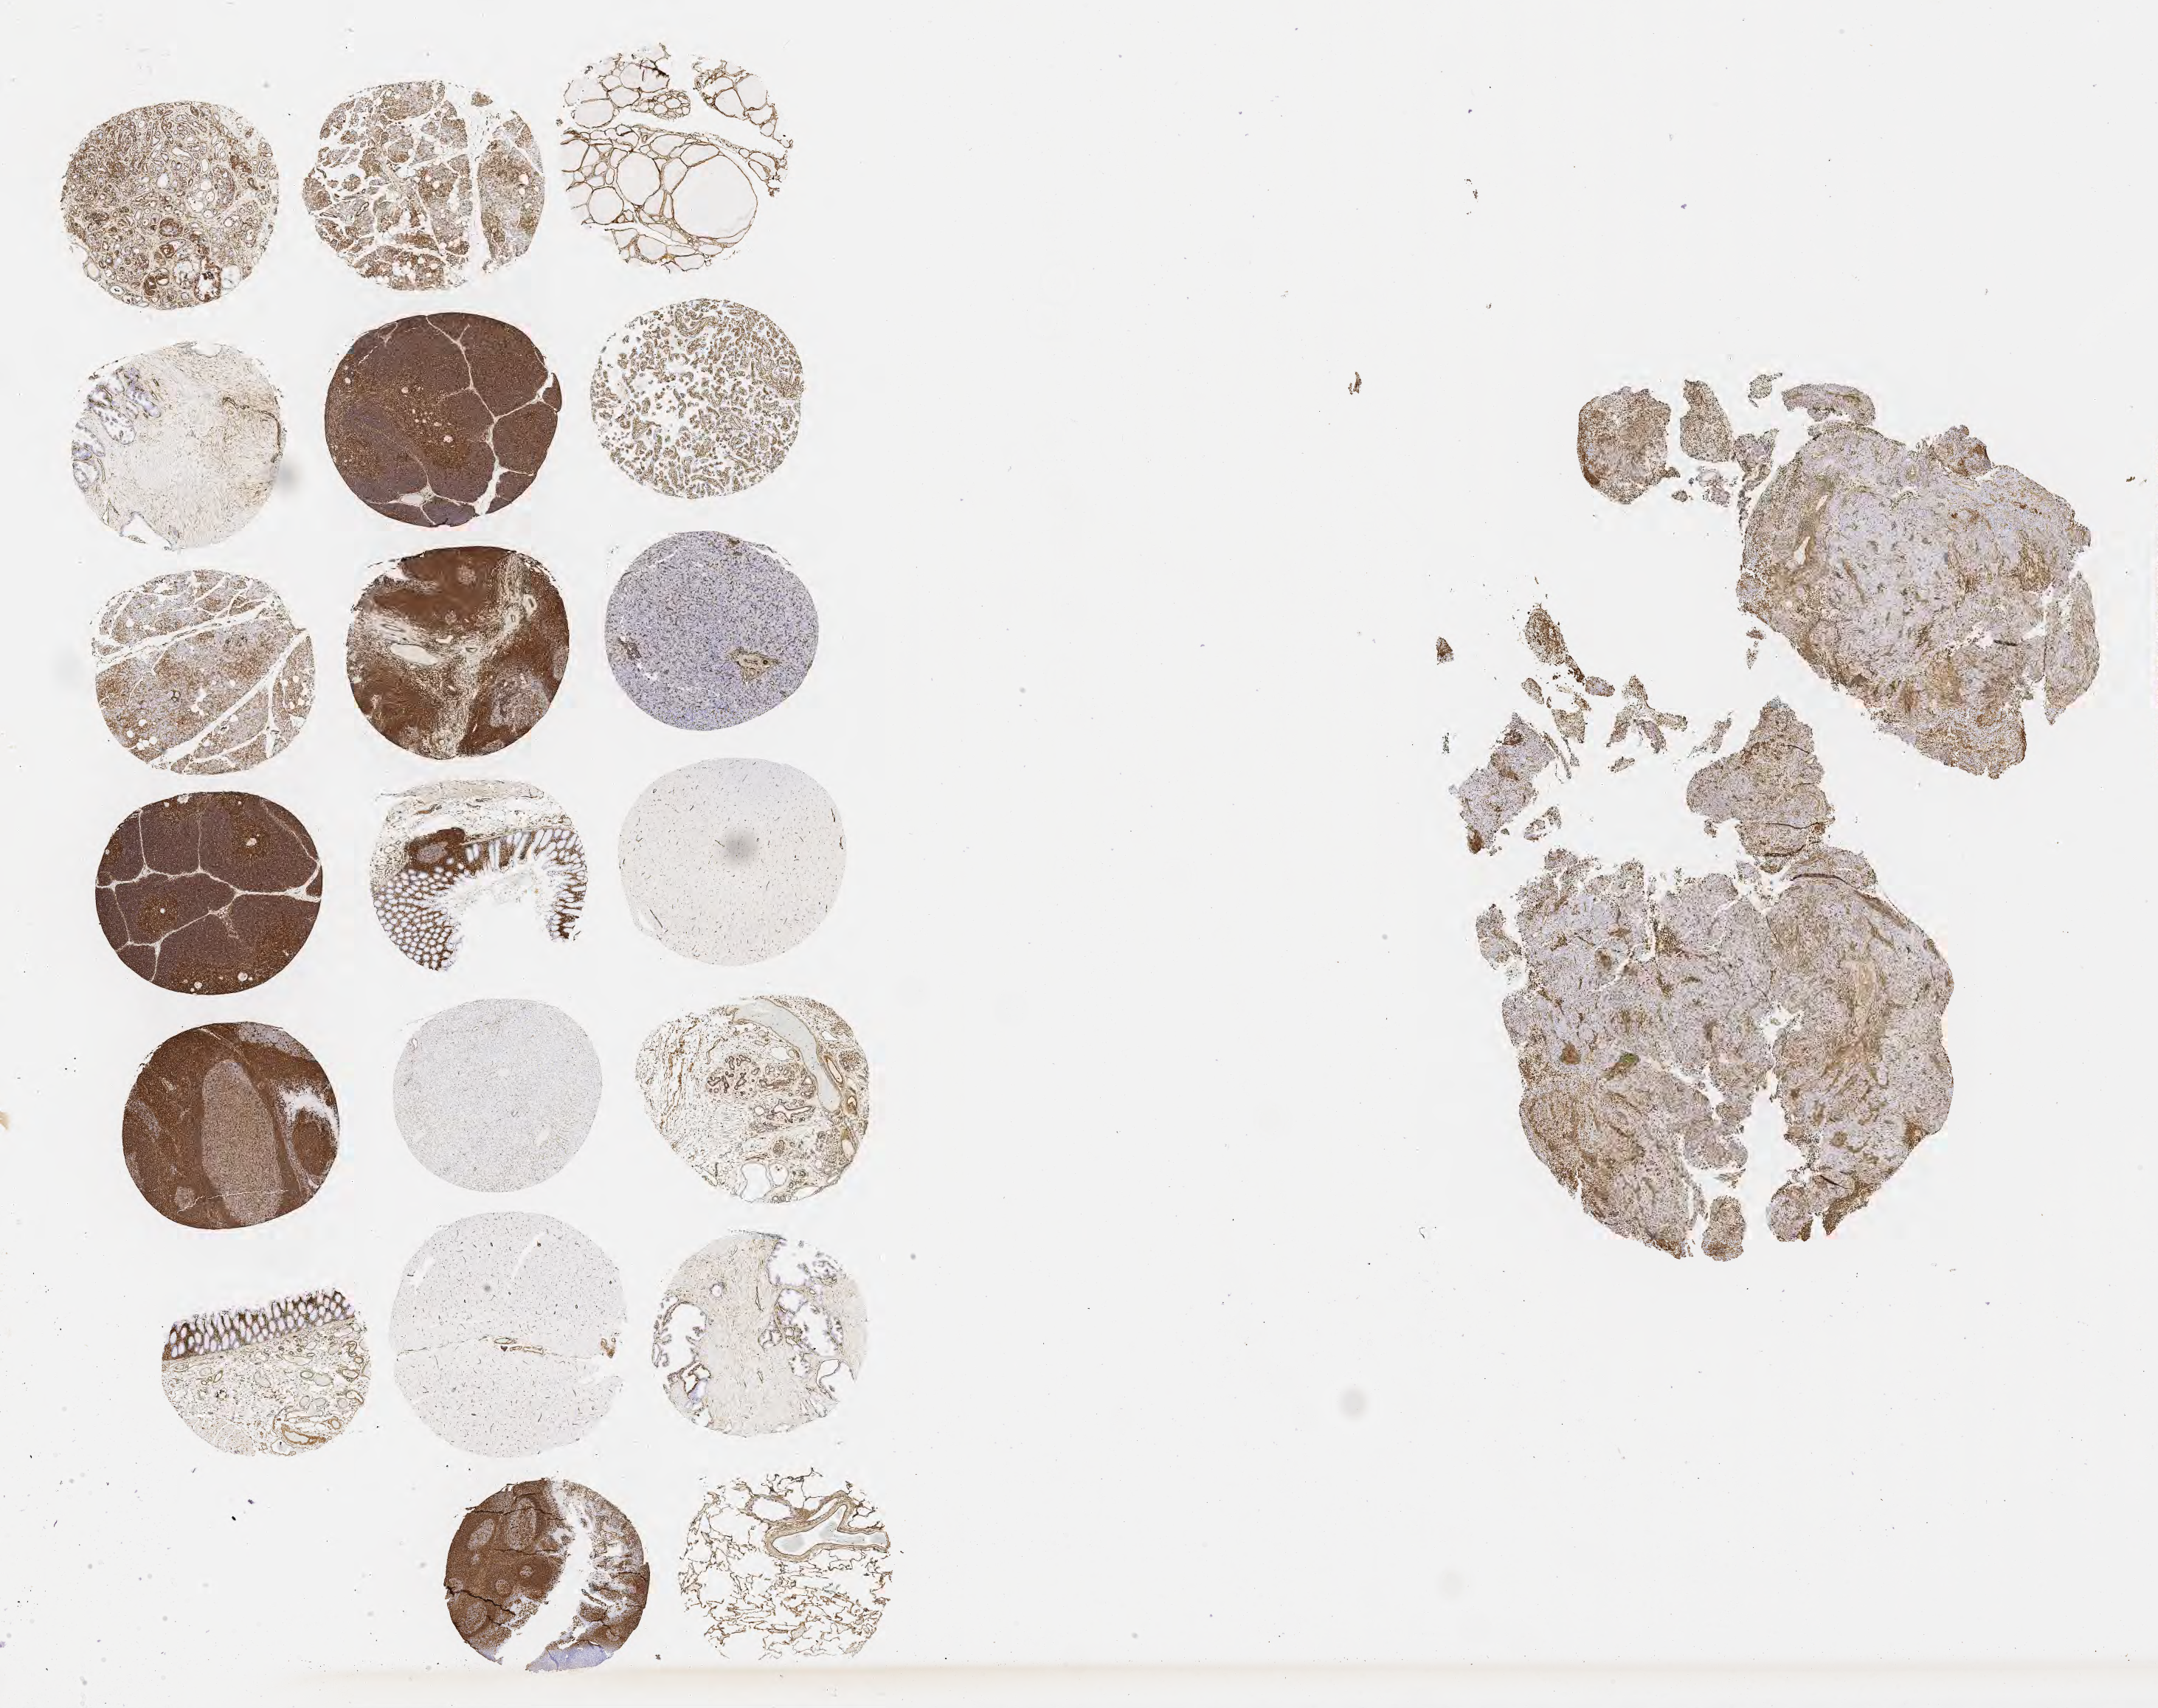
Whole-slide image, immunohistochemical stain for vimentin, a low-resolution overview of the entire scanned area, about 23.6 x 18.7 mm, tumor tissue, anatomic site: cervix. Patient: female, 70 years old.
- diagnosis: Squamous cell carcinoma, large cell, nonkeratinizing, NOS